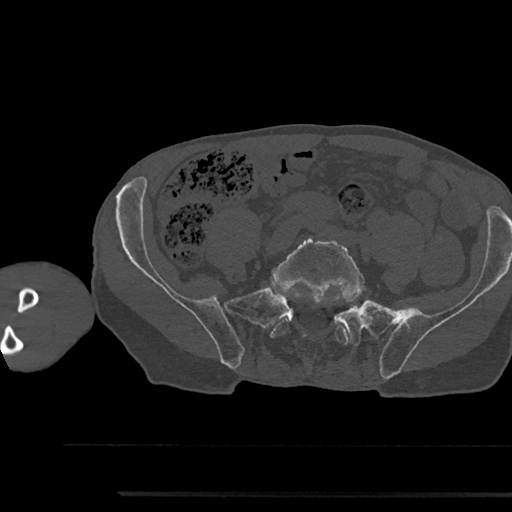
CT including the spine, one axial slice; slice 319 of 797 in the series (ordered by position); bone window (W 1800 / L 400 HU); 512 × 512 image matrix, field of view 367 × 367 mm. Patient: male, 79 years. From the clinical record (not read from this slice): primary cancer: prostate.
Annotated regions visible in this slice (semi-automatically segmented with operator editing):
- L5 vertebra: bounding box <270,234,363,344> (left, top, right, bottom; pixels)